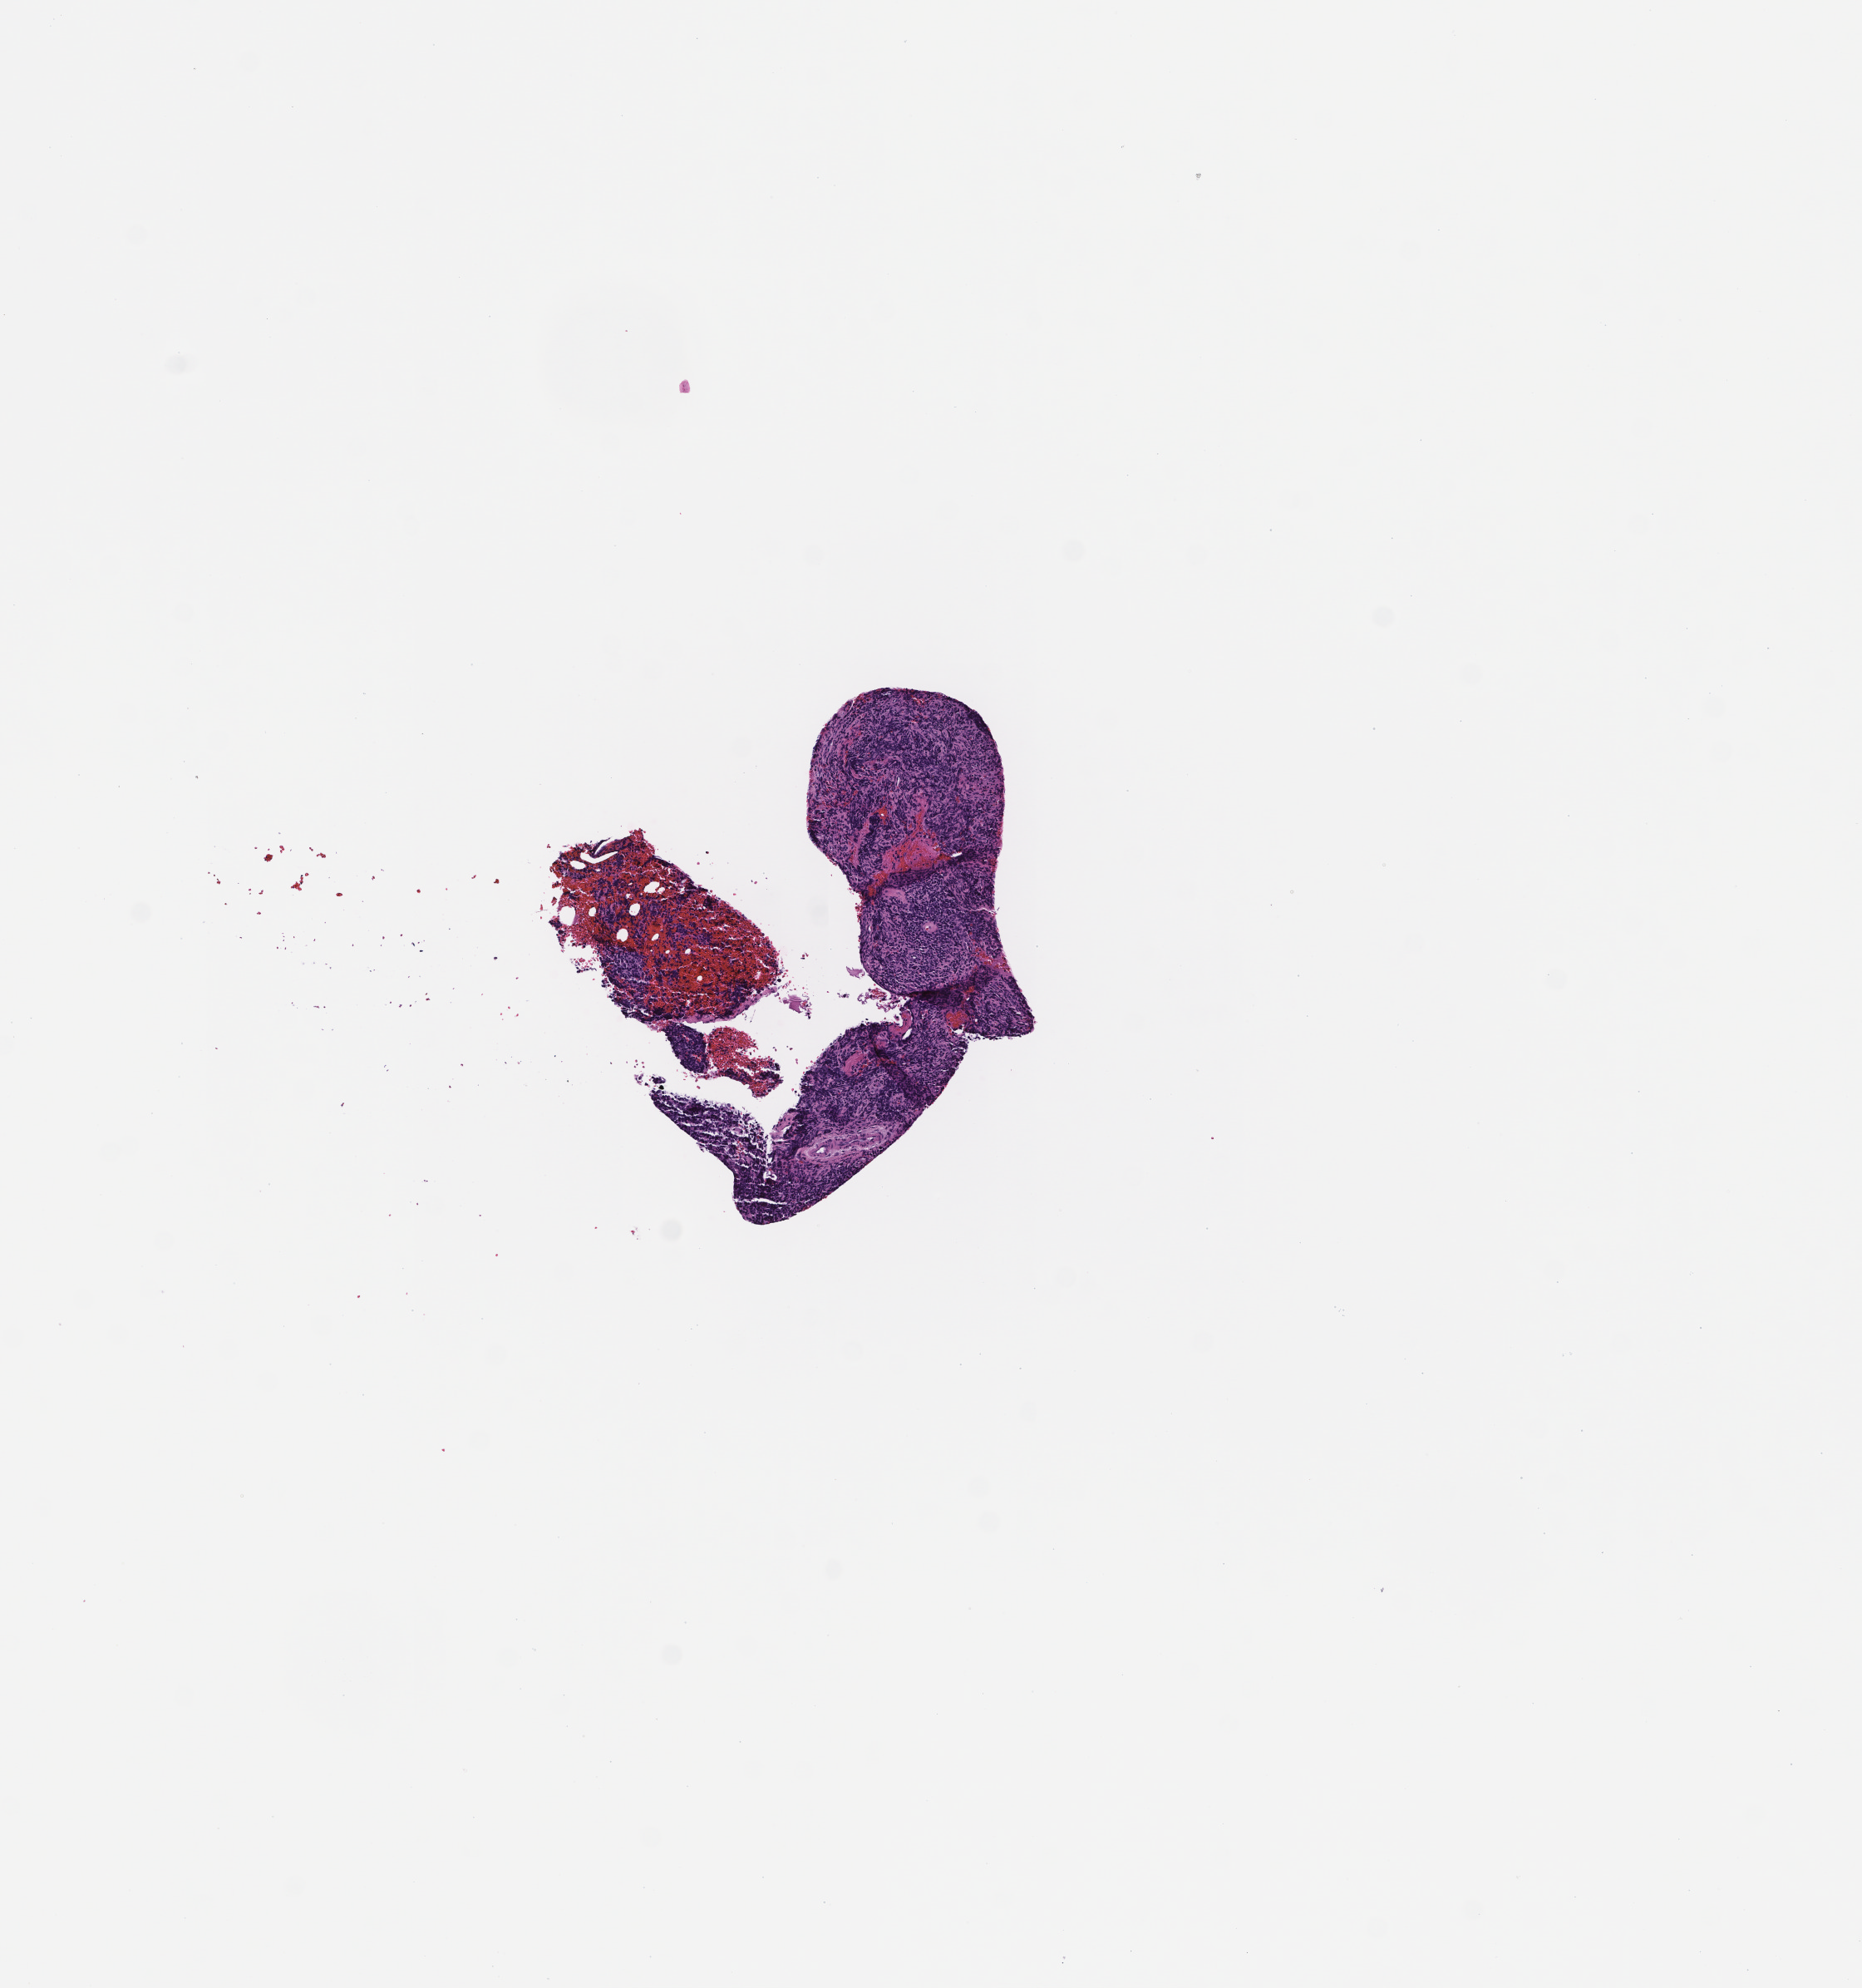
Digitized hematoxylin and eosin (H&E)-stained section, shown as a low-resolution overview of the whole scanned area (about 4.5 x 4.8 mm); FFPE section; collected at disease progression. Male patient.
This section: metastatic tumor tissue. Primary diagnosis of the patient: Melanoma.